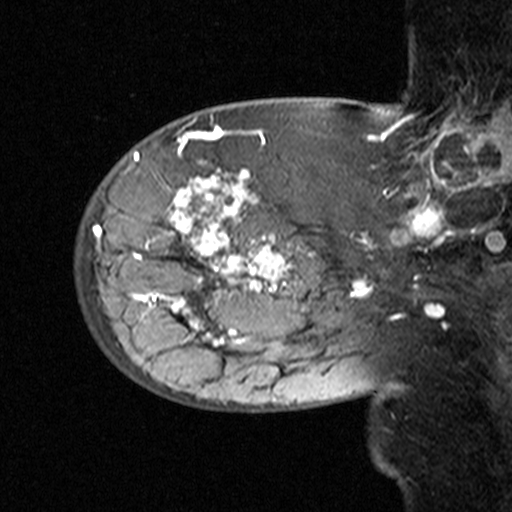
Breast MRI (dynamic contrast-enhanced), one sagittal slice; position 13 of 44 along the scan axis; dynamic contrast-enhanced study with each time point stored as its own series, time point 2 of 3 at this slice position (early post-contrast, ordered by acquisition time); 1.5 T; TE 4.5 ms, TR 11 ms; 3 mm slice thickness; 512 × 512 image matrix, field of view 200 × 200 mm. Patient: female, 53 years. From the clinical record (not read from this slice): setting: breast cancer imaged before/during neoadjuvant chemotherapy; receptor status: HR-positive, HER2-negative.
Annotated regions visible in this slice (semi-automatic segmentation, software-assisted and operator-edited):
- analysis volume of interest (the breast-tissue region the enhancement analysis was run in; not a lesion): bounding box <76,140,311,353> (left, top, right, bottom; pixels)
- tumour enhancement mask (voxels above the 90 % enhancement threshold inside the analysis volume of interest): <133,162,306,344>